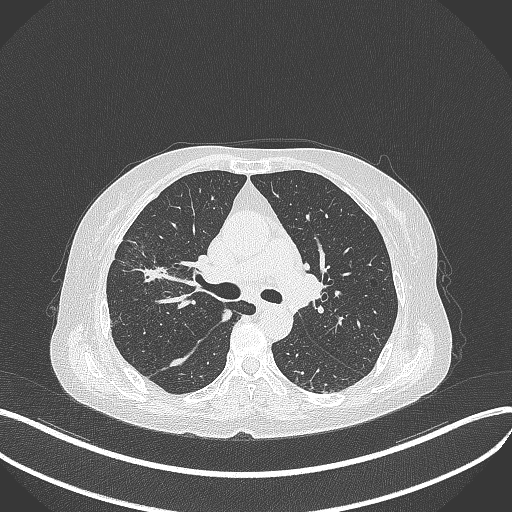
Chest CT, one axial slice. Position 252 of 429 along the scan axis. Reconstruction kernel B70f. 120 kVp. Lung window (W 1500 / L -600 HU). 512 × 512 image matrix. Patient: female, 69 years. From the clinical record (not read from this slice): clinical TNM (as recorded): T1b N3 M0.
Outlined on this slice (rectangle marked by the reading radiologist):
- lung tumour (recorded histology: small cell carcinoma): bounding box [x1, y1, x2, y2] px = [125, 259, 173, 286]